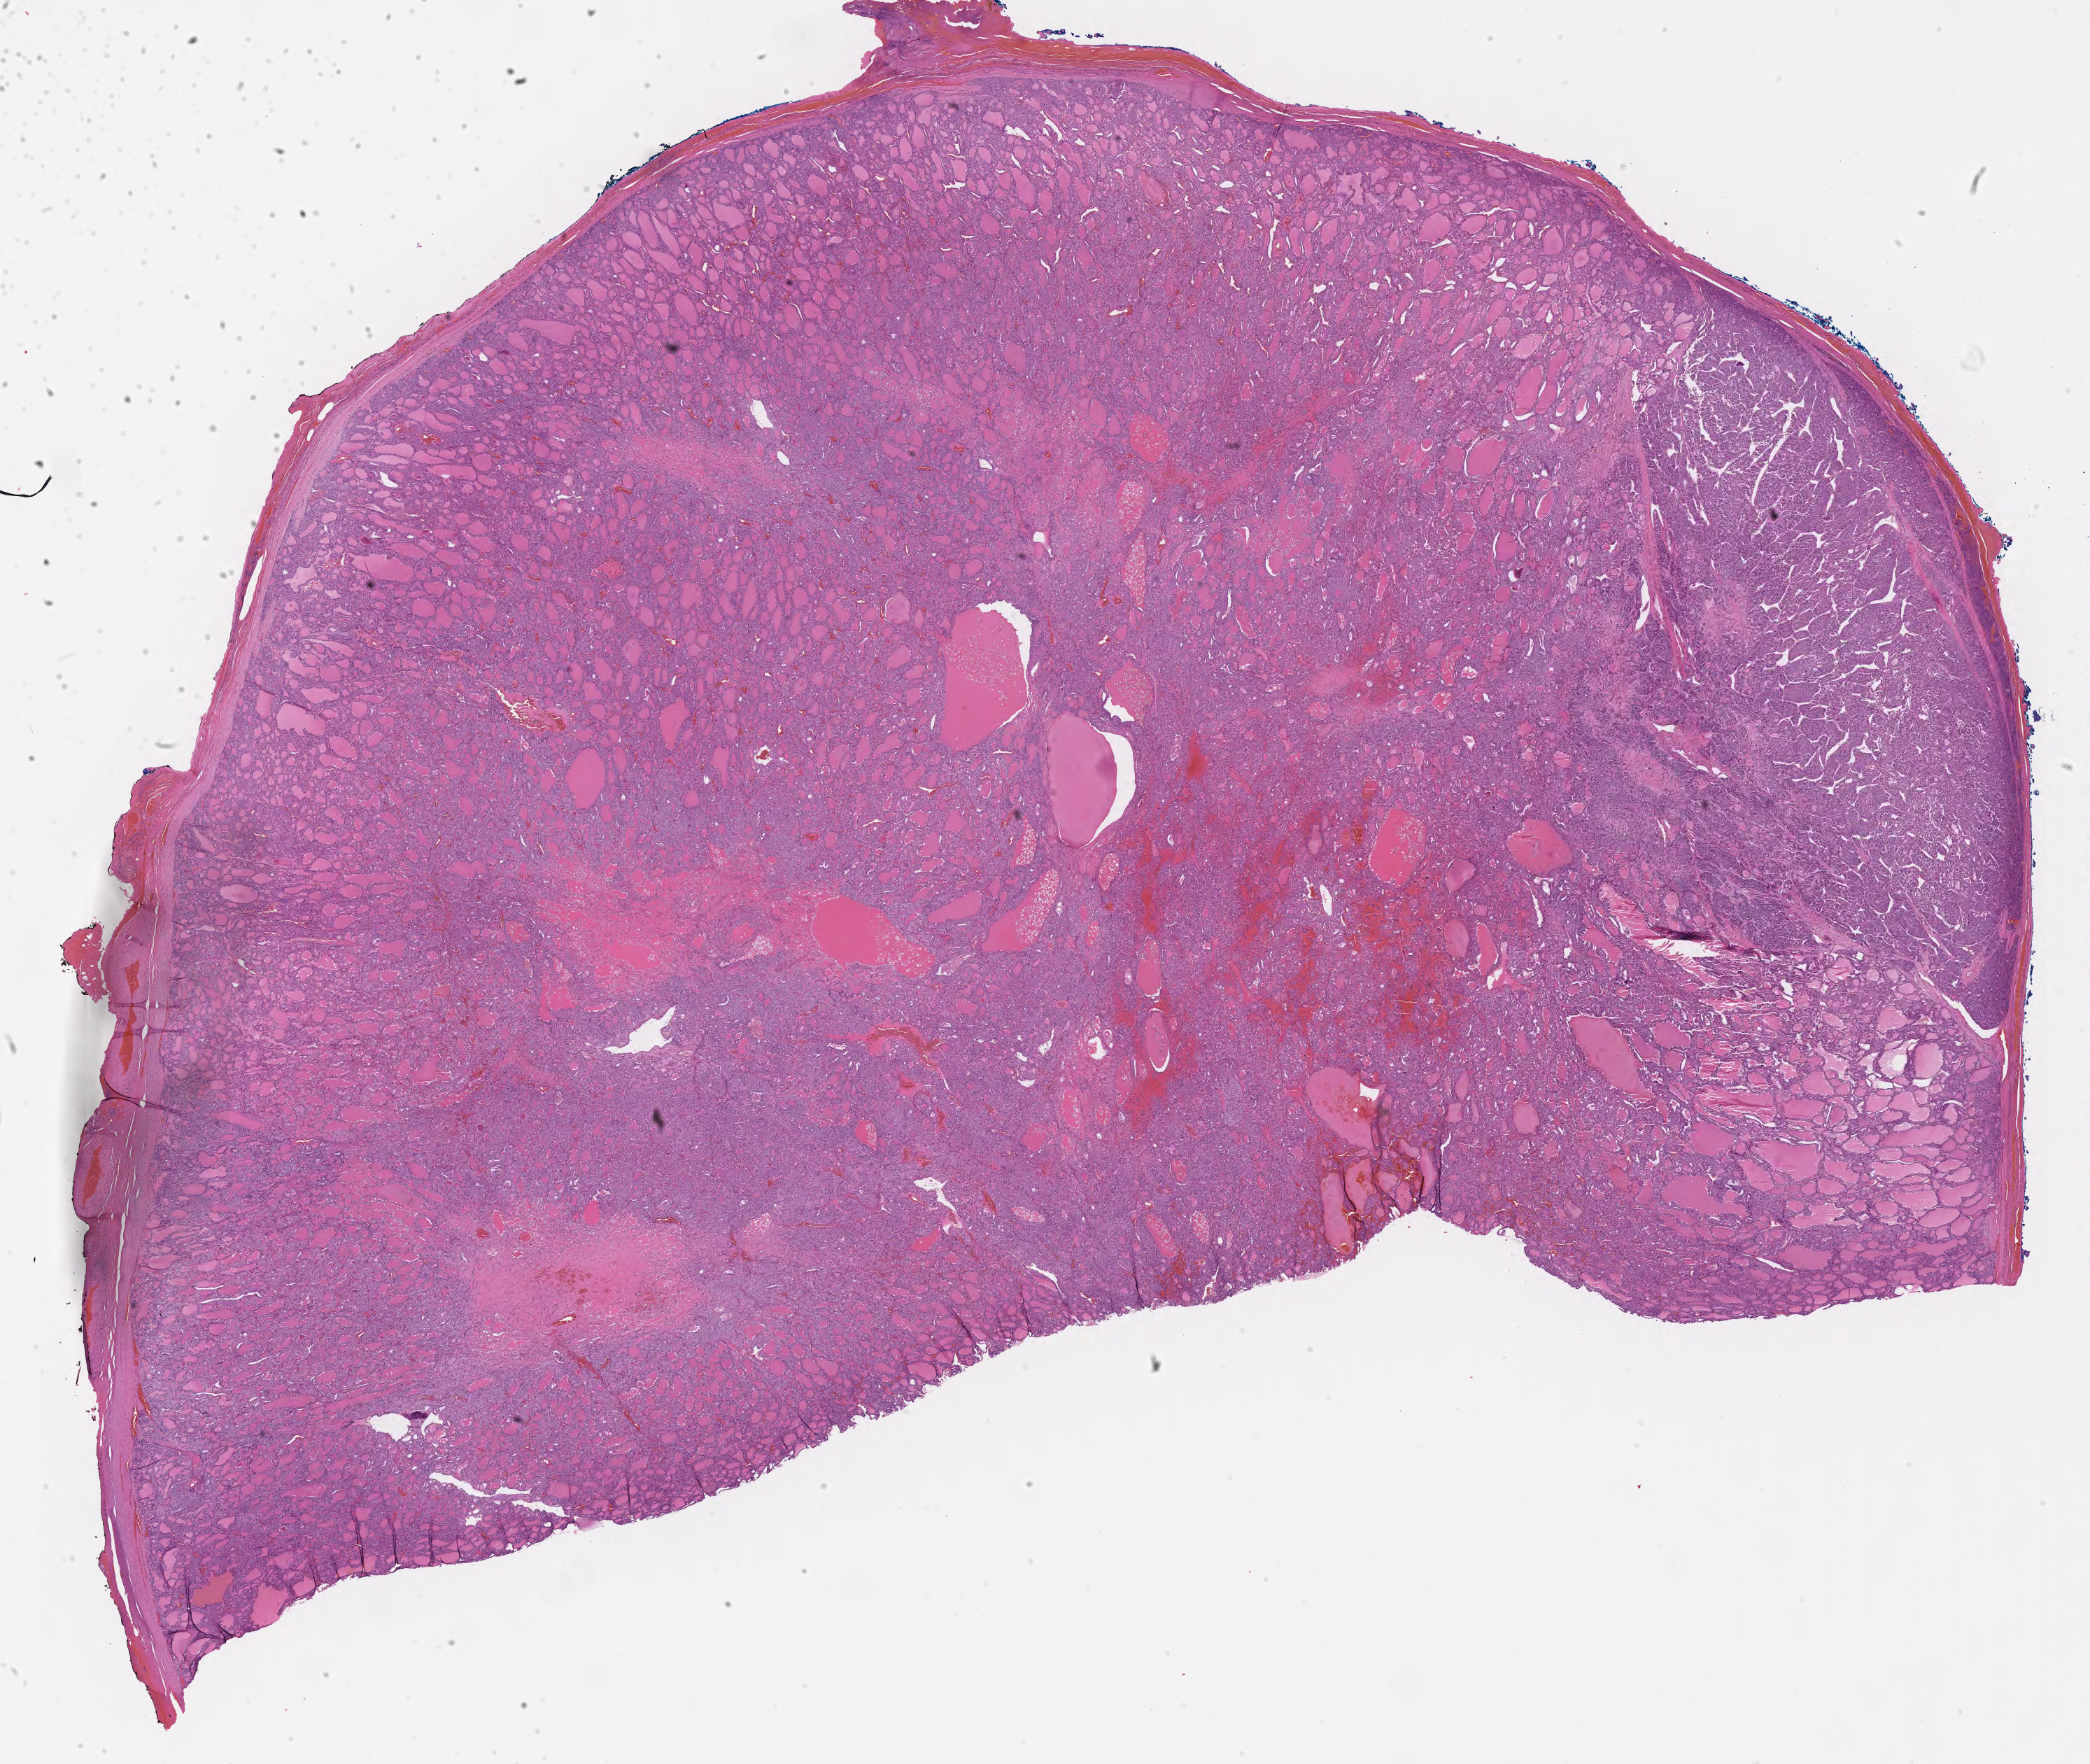
Whole-slide image, H&E stain of tumor tissue from the thyroid — low-resolution overview of the scanned area, about 24.2 x 20.4 mm, formalin-fixed paraffin-embedded section. Patient: male, age 179 months (14 years 11 months).
Diagnosis (ICD-O-3 morphology term): Carcinoma, NOS.